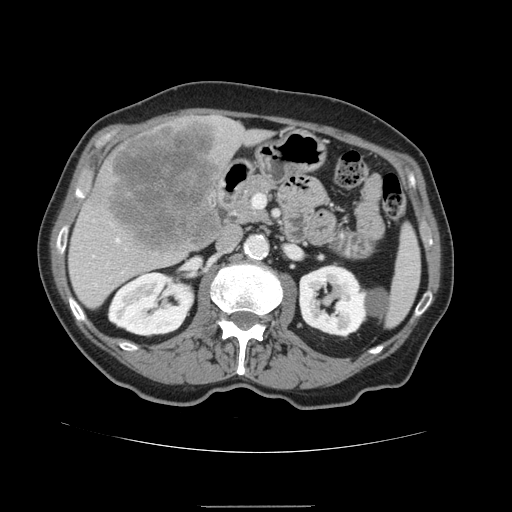
Contrast-enhanced abdominal CT, one axial slice. Position 70 of 168 along the scan axis. Intravenous contrast given. Soft-tissue window (W 400 / L 40 HU). 2.5 mm slice thickness. 512 × 512 image matrix, field of view 386 × 386 mm. Male patient, age 74 years. Case-level facts recorded for this patient, not image findings: diagnosis: colorectal cancer liver metastases, imaged before liver resection; multiple liver metastases: no; largest metastasis: 14.5 cm; chemotherapy before resection: no.
Structures marked on this image (outlined manually by an expert reader):
- hepatic veins: bounding box <117,239,119,241> (left, top, right, bottom; pixels)
- liver: <68,115,274,310>
- planned liver remnant (the part of the liver to remain after resection): <70,129,274,309>
- liver metastasis: <109,120,221,251>